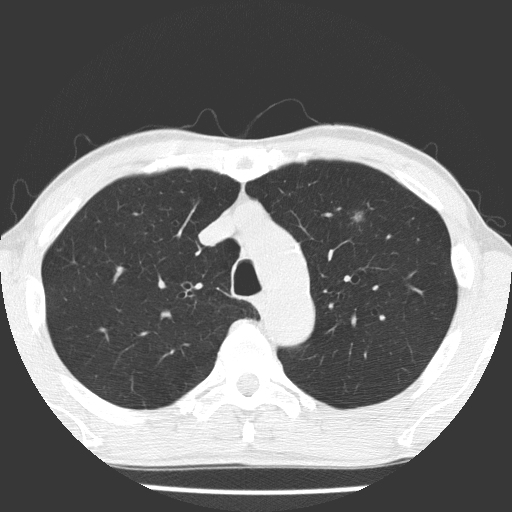
Low-dose screening chest CT, one axial slice. Slice 128 of 177 in the series (ordered by position). 120 kVp. Lung window (W 1500 / L -600 HU). 512 × 512 image matrix, field of view 305 × 305 mm.
Outlined on this slice (outlined manually by an expert reader):
- lesion 1 (tumor, upper lobe of left lung): bounding box [x1, y1, x2, y2] px = [354, 212, 365, 223]